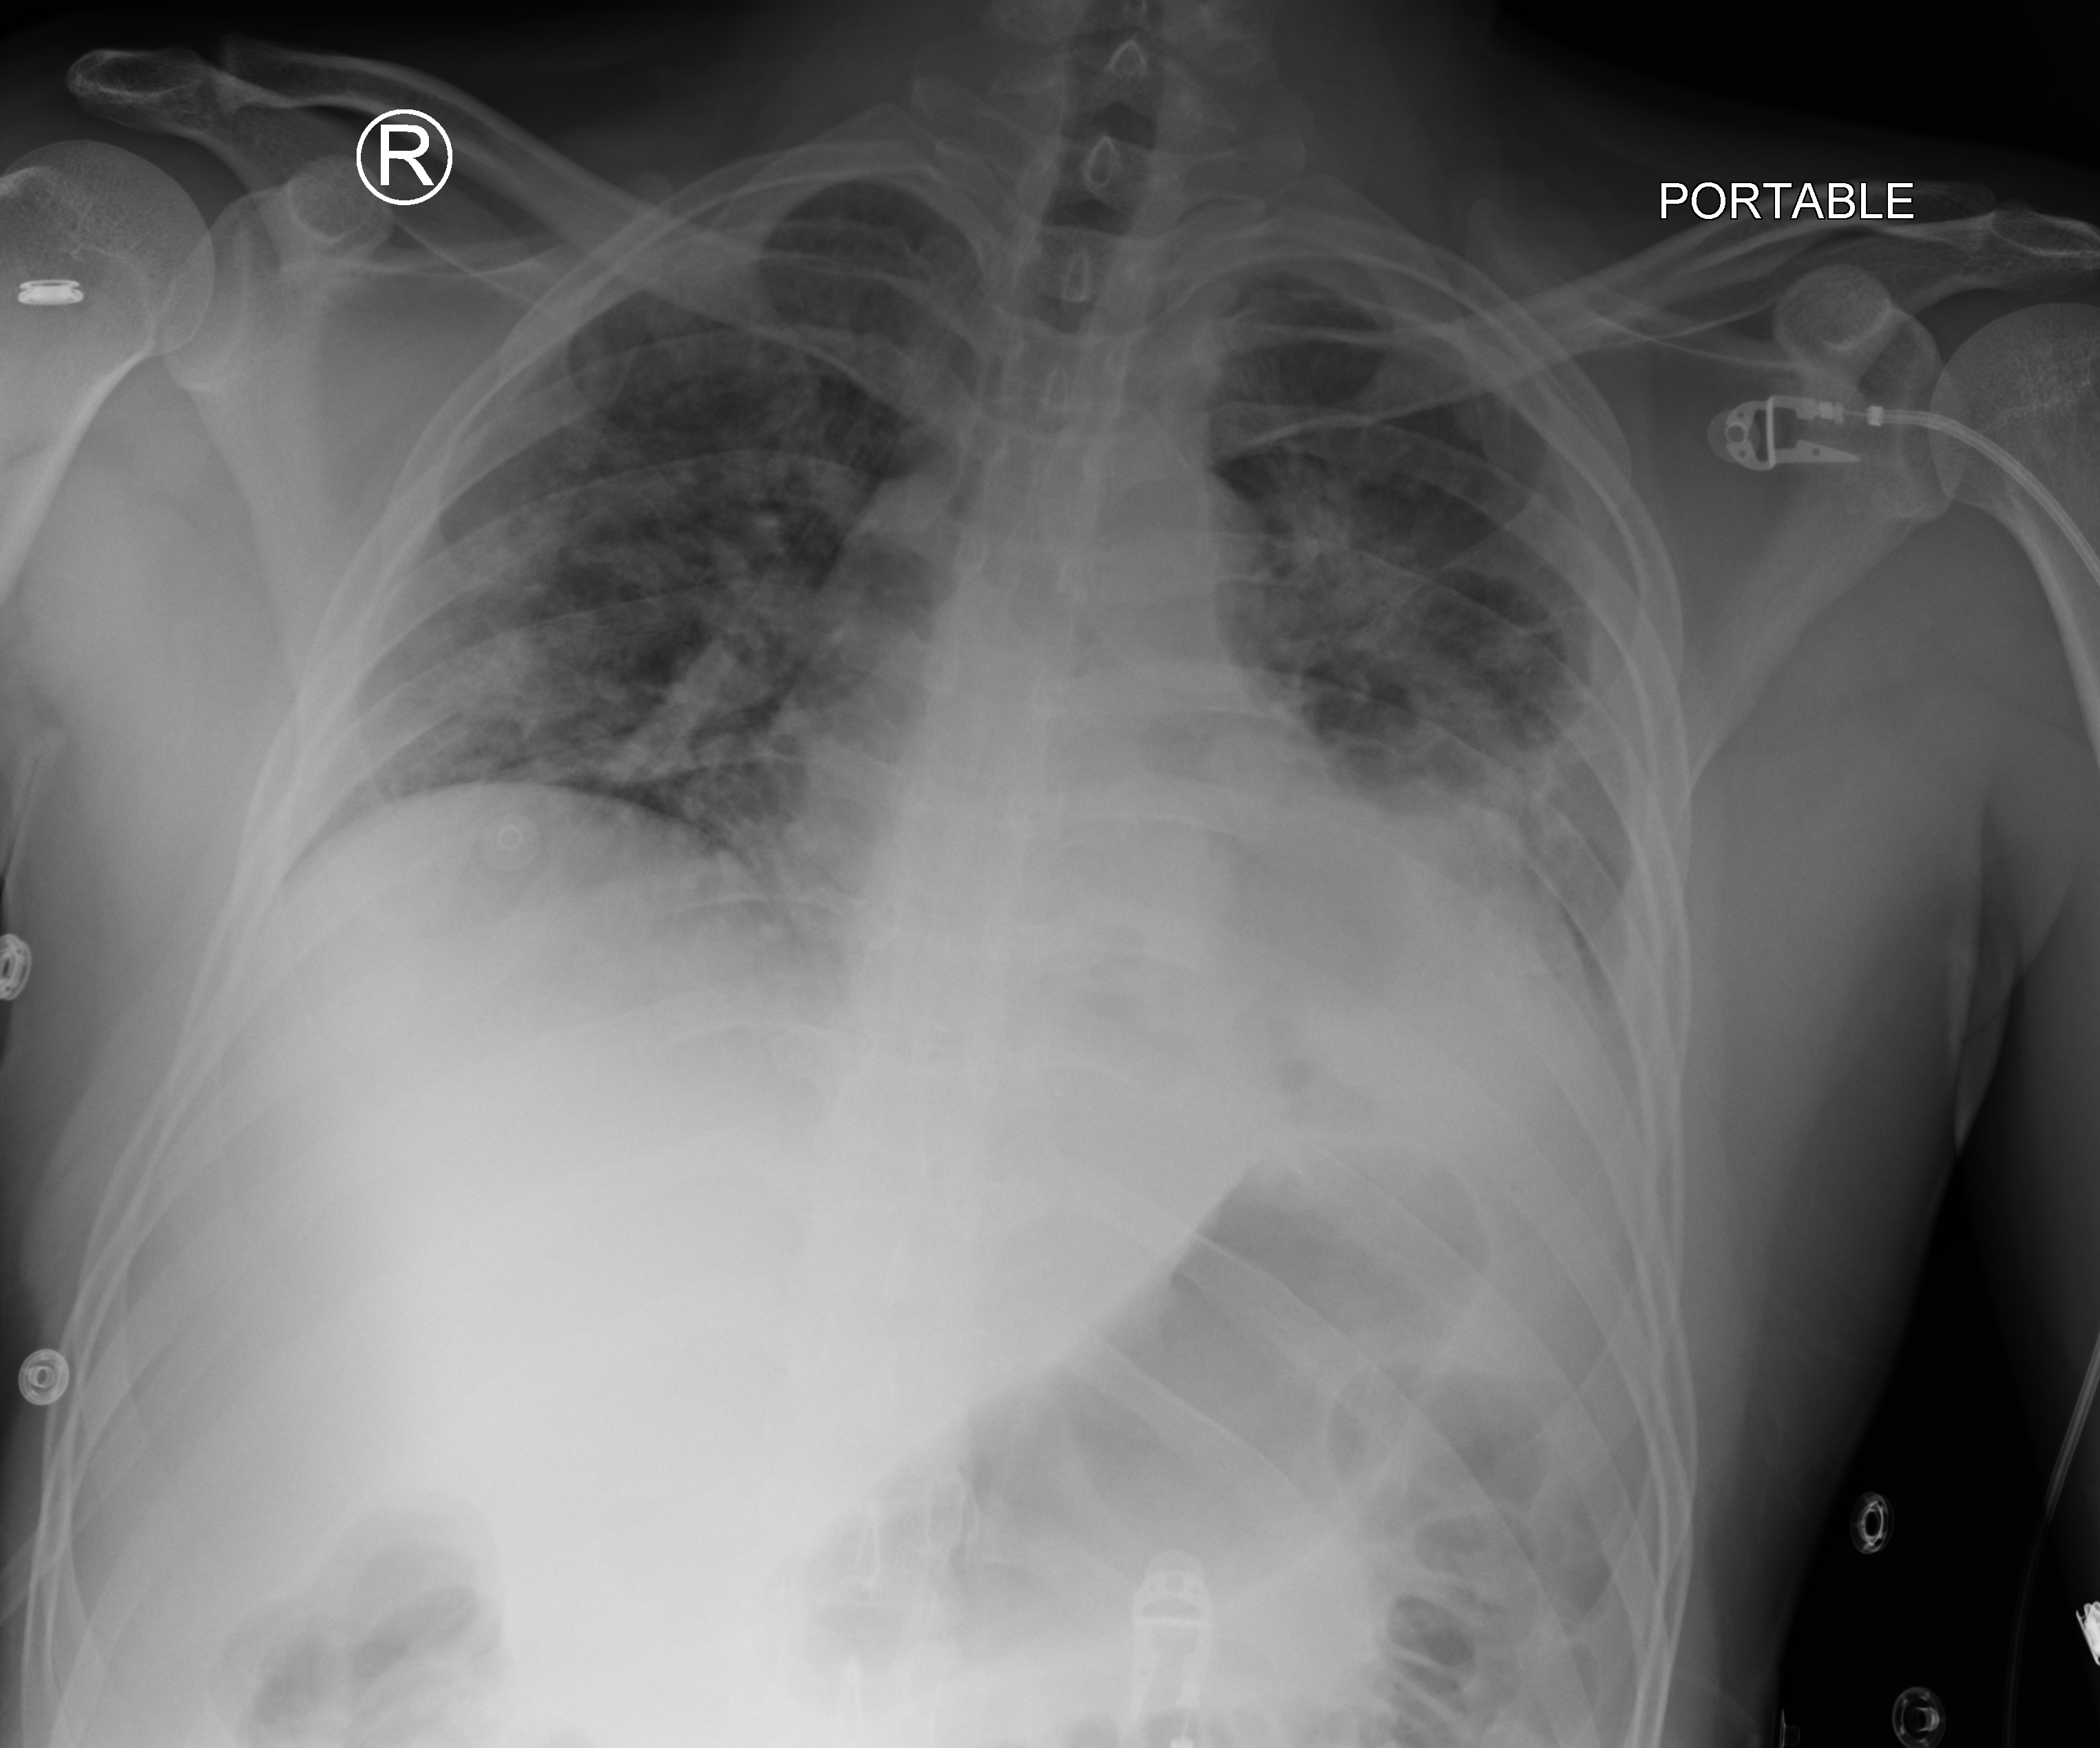
Bedside chest radiograph (computed radiography); anteroposterior (AP) projection. Male patient hospitalised with COVID-19, age 18–59 years.
From the hospital-stay record, not from the radiograph (when in the stay this image was taken is not recorded): length of hospital stay: 31 days; admitted to intensive care during this hospital stay: yes; smoking status (admission record): never.